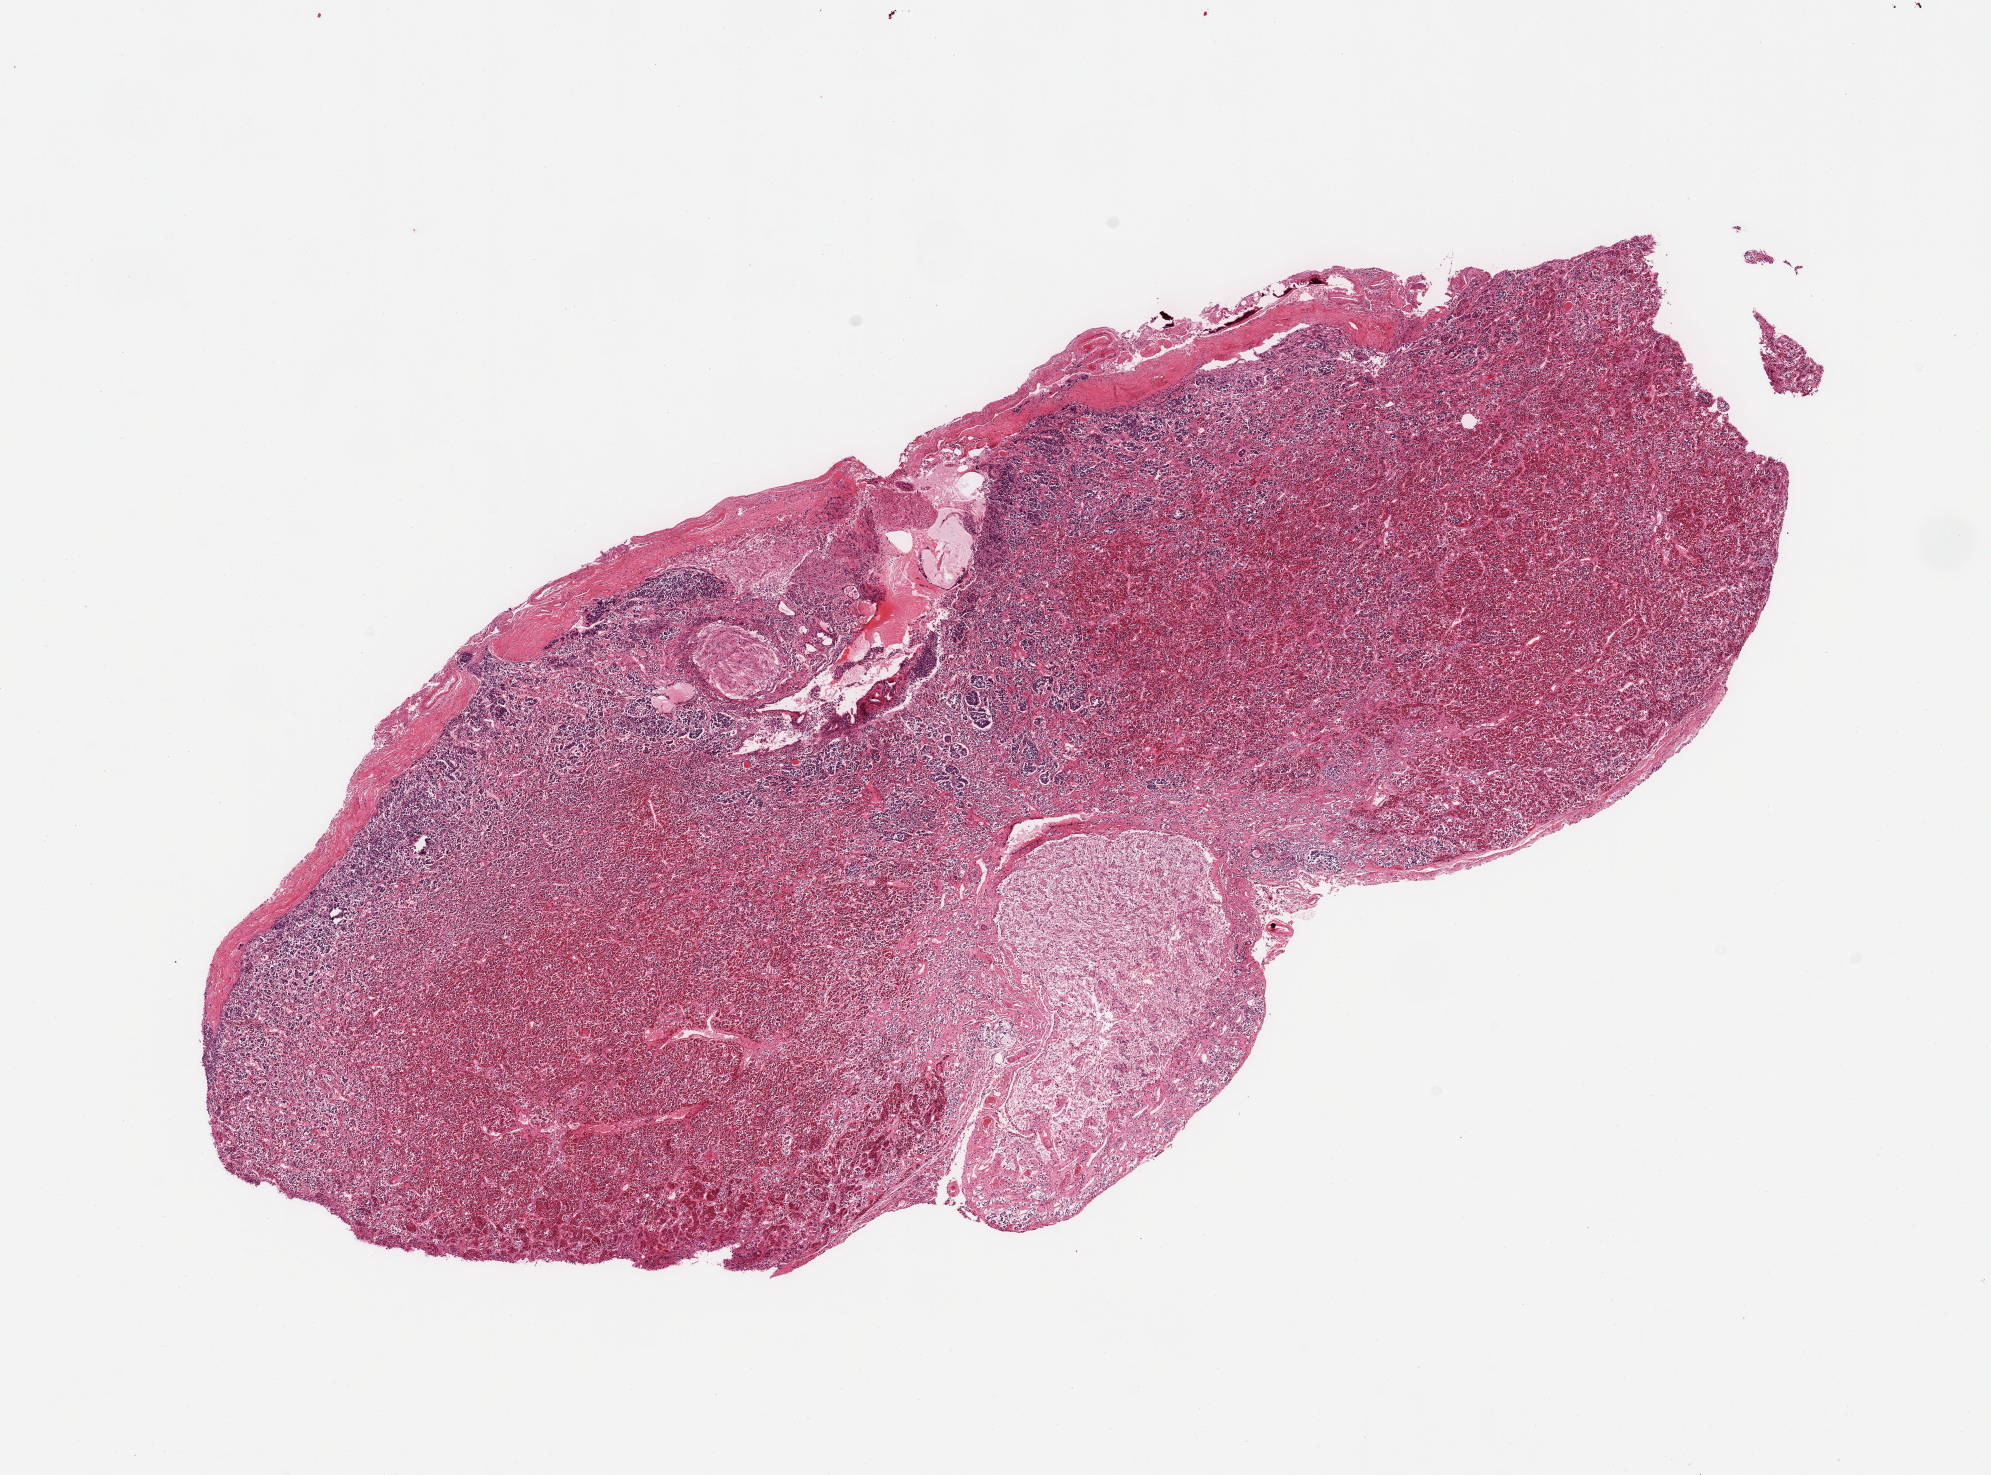
Haematoxylin and eosin whole-slide image — a low-resolution overview of the entire scanned area, about 15.8 x 11.7 mm (acquisition: 20x scan), PAXgene-fixed, paraffin-embedded tissue, target tissue: pituitary, tissue donor sample. Donor sex: female.
* reviewer comment on this tissue sample: 1 piece; anterior & posterior lobes